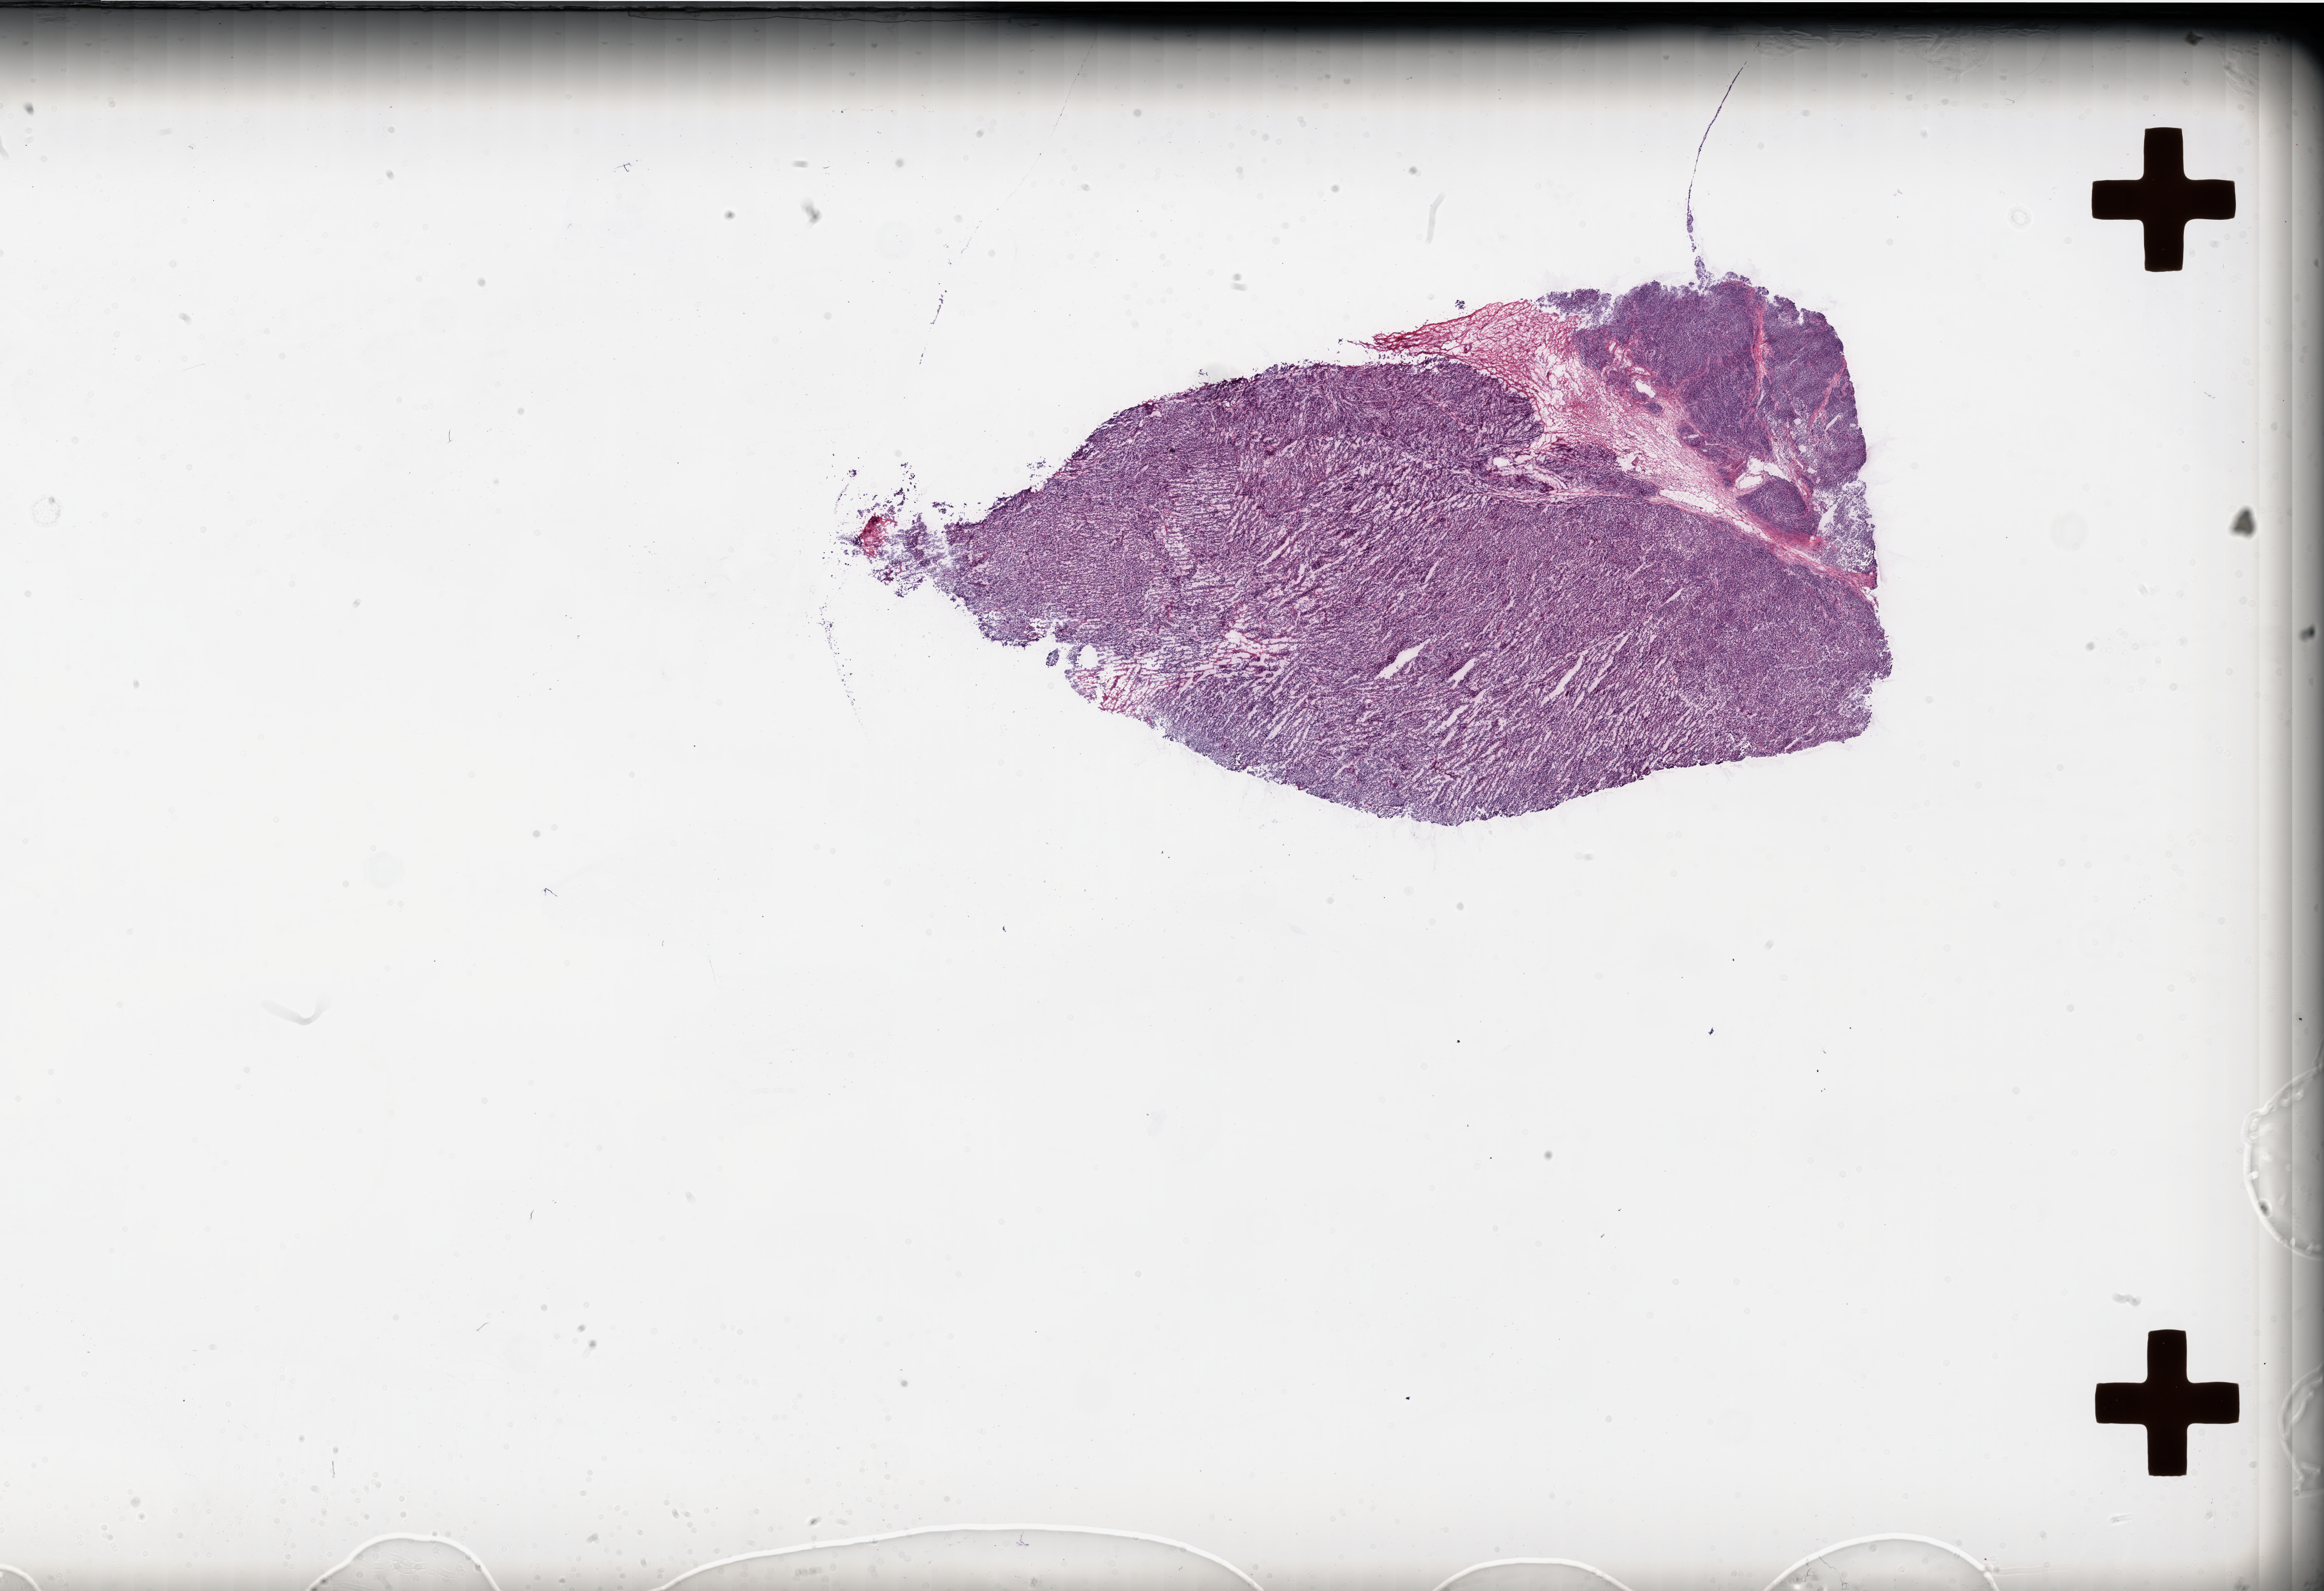
Digitized H&E-stained tissue section (whole slide) — shown as a low-resolution overview of the whole scanned area (about 33.7 x 23.1 mm), frozen section, ovary, primary tumour sample. Patient: female, age at initial diagnosis 46 years. Histologic grade: G3 (poorly differentiated). Slide review estimates, as recorded: tumour cells 95%, tumour nuclei 98%, normal cells 0%, stromal cells 5%, necrosis 0%.
Pathologic diagnosis: Serous cystadenocarcinoma, NOS. FIGO stage: IIIC.